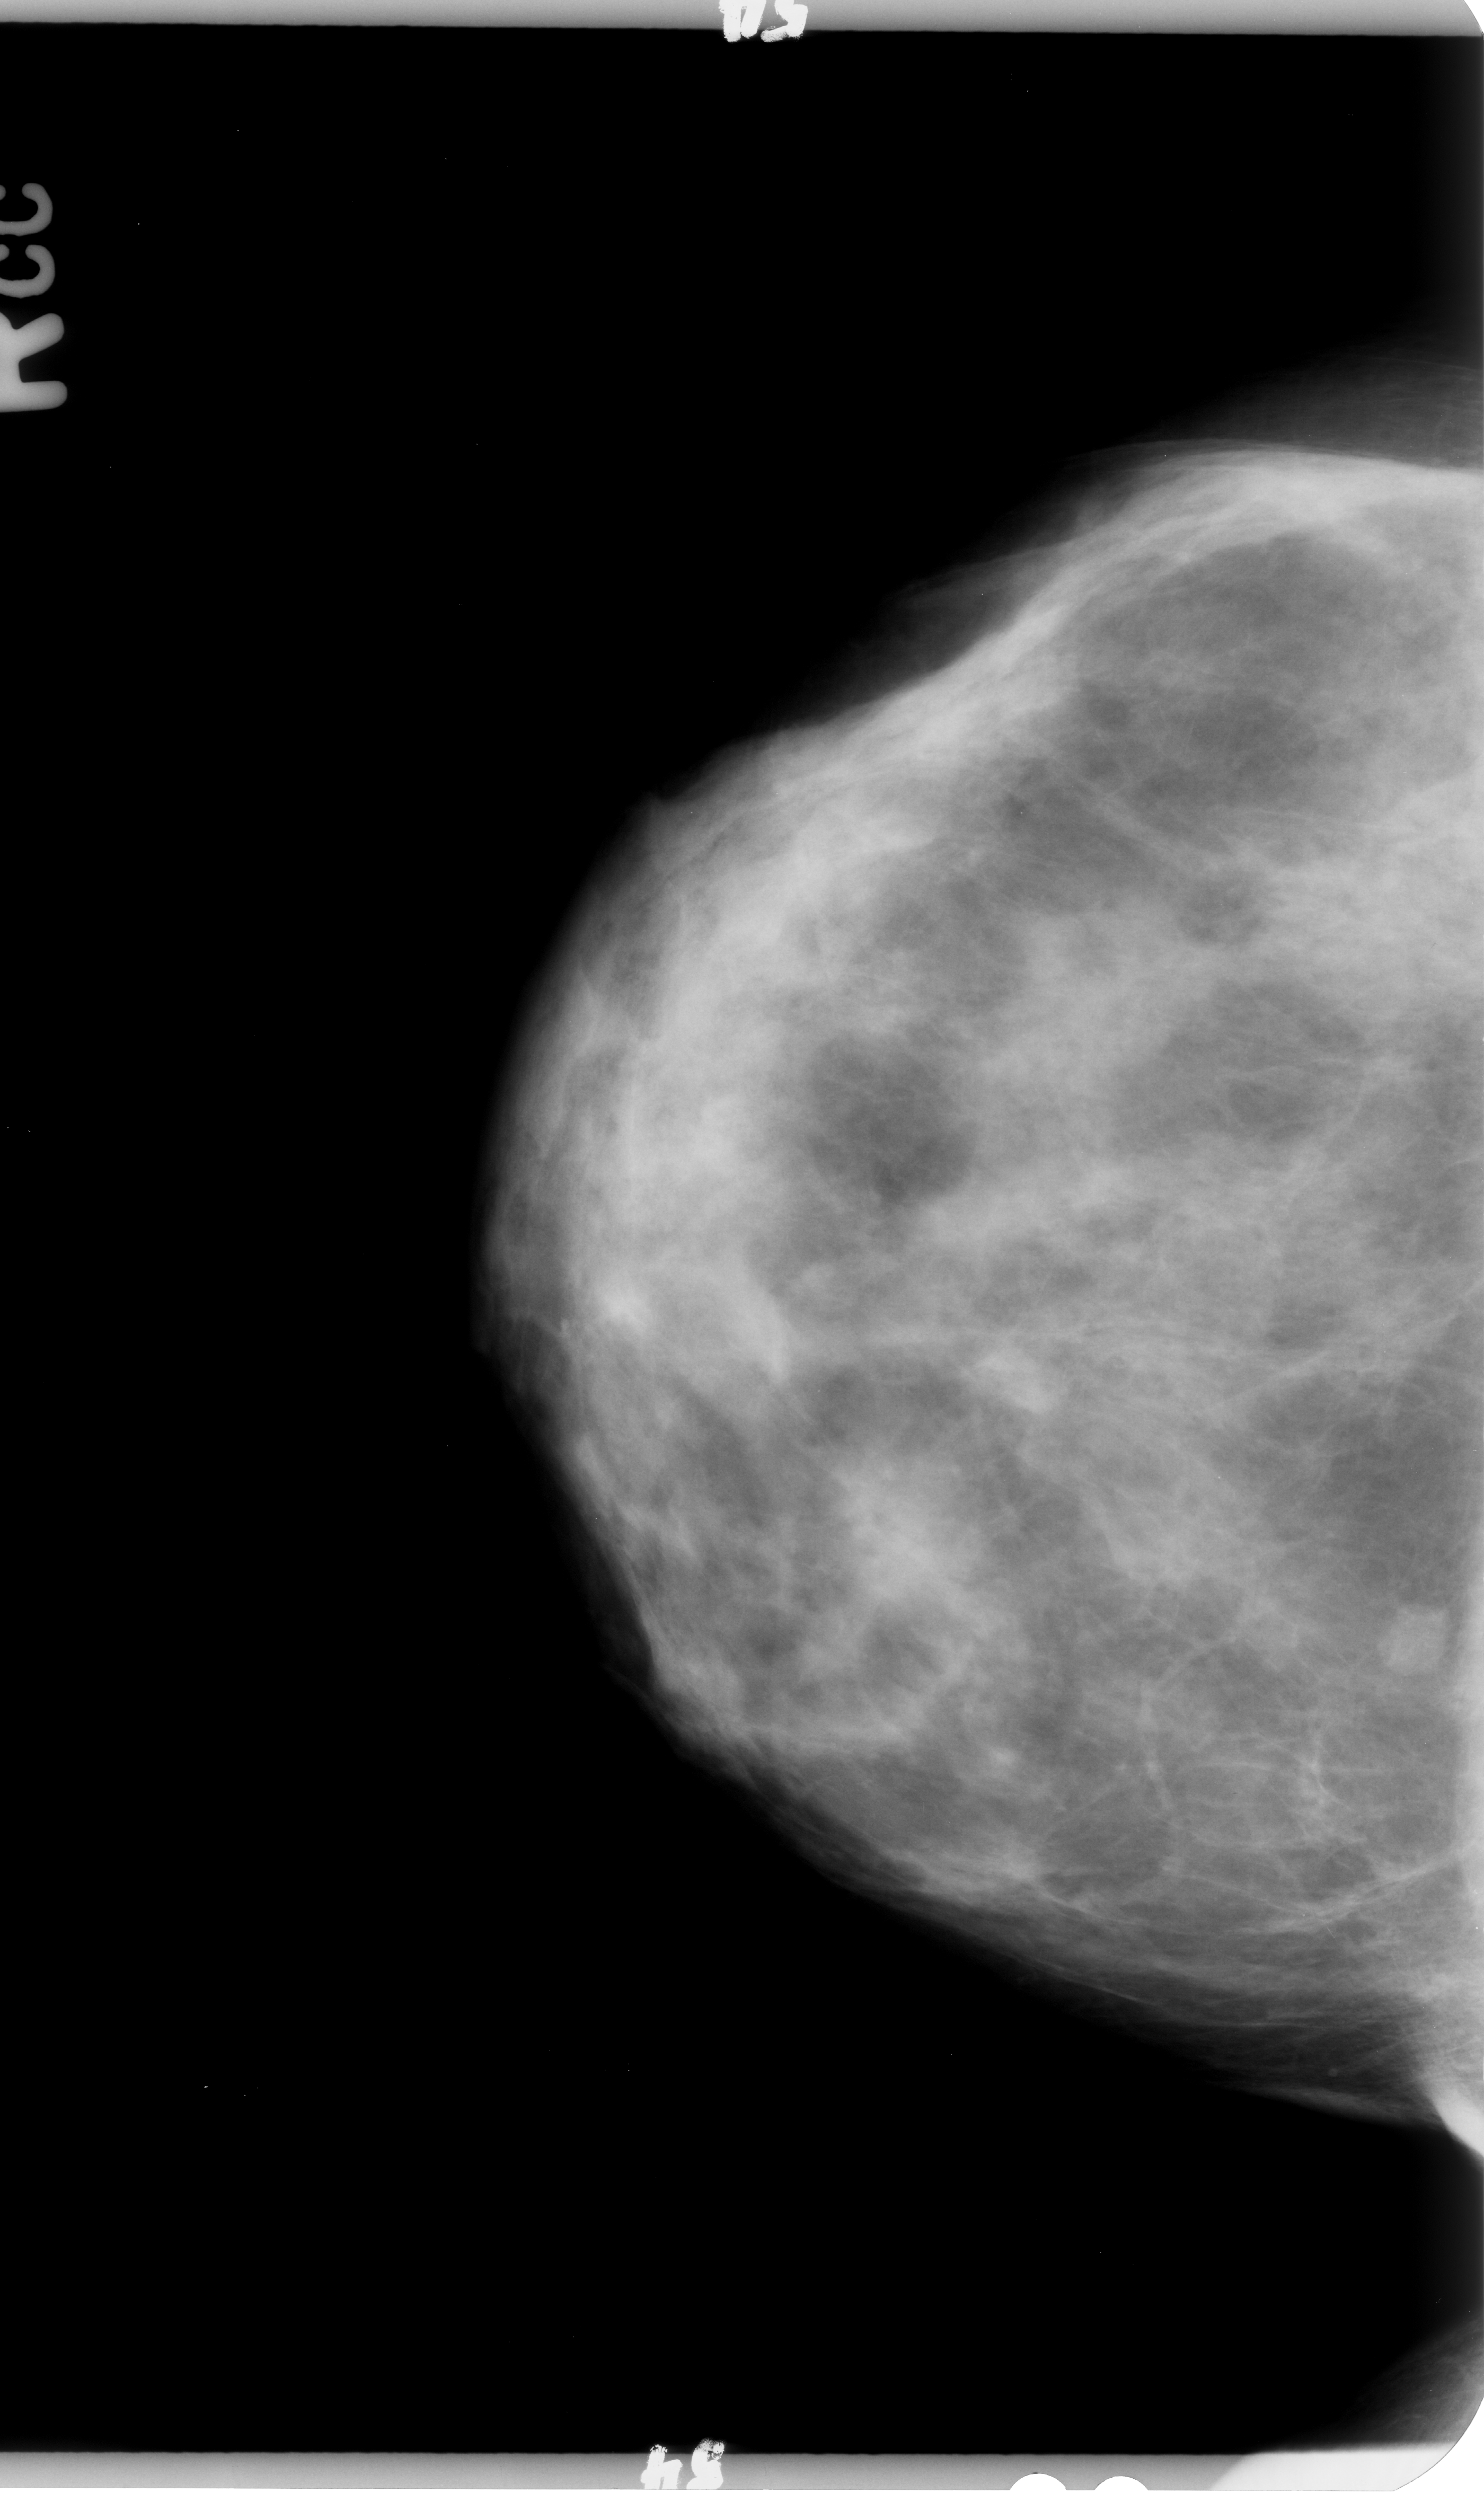
Scanned film-screen mammogram, right breast, CC view, BI-RADS breast density category 2 (scale 1–4).
Mass, shape lobulated, margins circumscribed; BI-RADS assessment category 4; subtlety rating 4 on a 1 (subtle) to 5 (obvious) scale; pathology result (as recorded, not read from the image): benign.